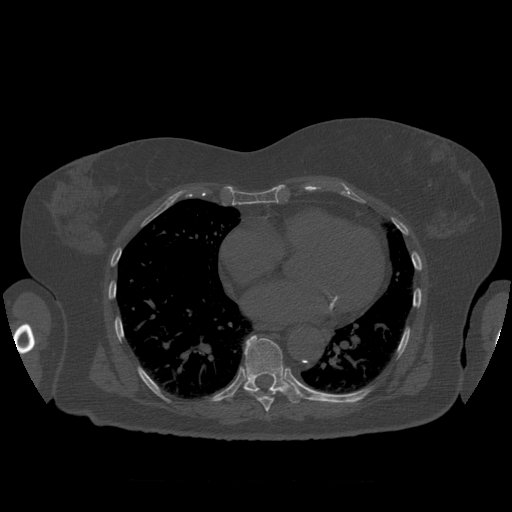
CT including the spine, one axial slice. Slice 368 of 399 in the series (ordered by position). 120 kVp. Bone window (W 1800 / L 400 HU). 512 × 512 image matrix. Patient age 81 years. Case-level facts recorded for this patient, not image findings: primary cancer: renal.
Structures marked on this image (semi-automatic segmentation, software-assisted and operator-edited):
- T8 vertebra: bounding box <244,389,277,412> (left, top, right, bottom; pixels)
- T9 vertebra: <244,336,302,404>